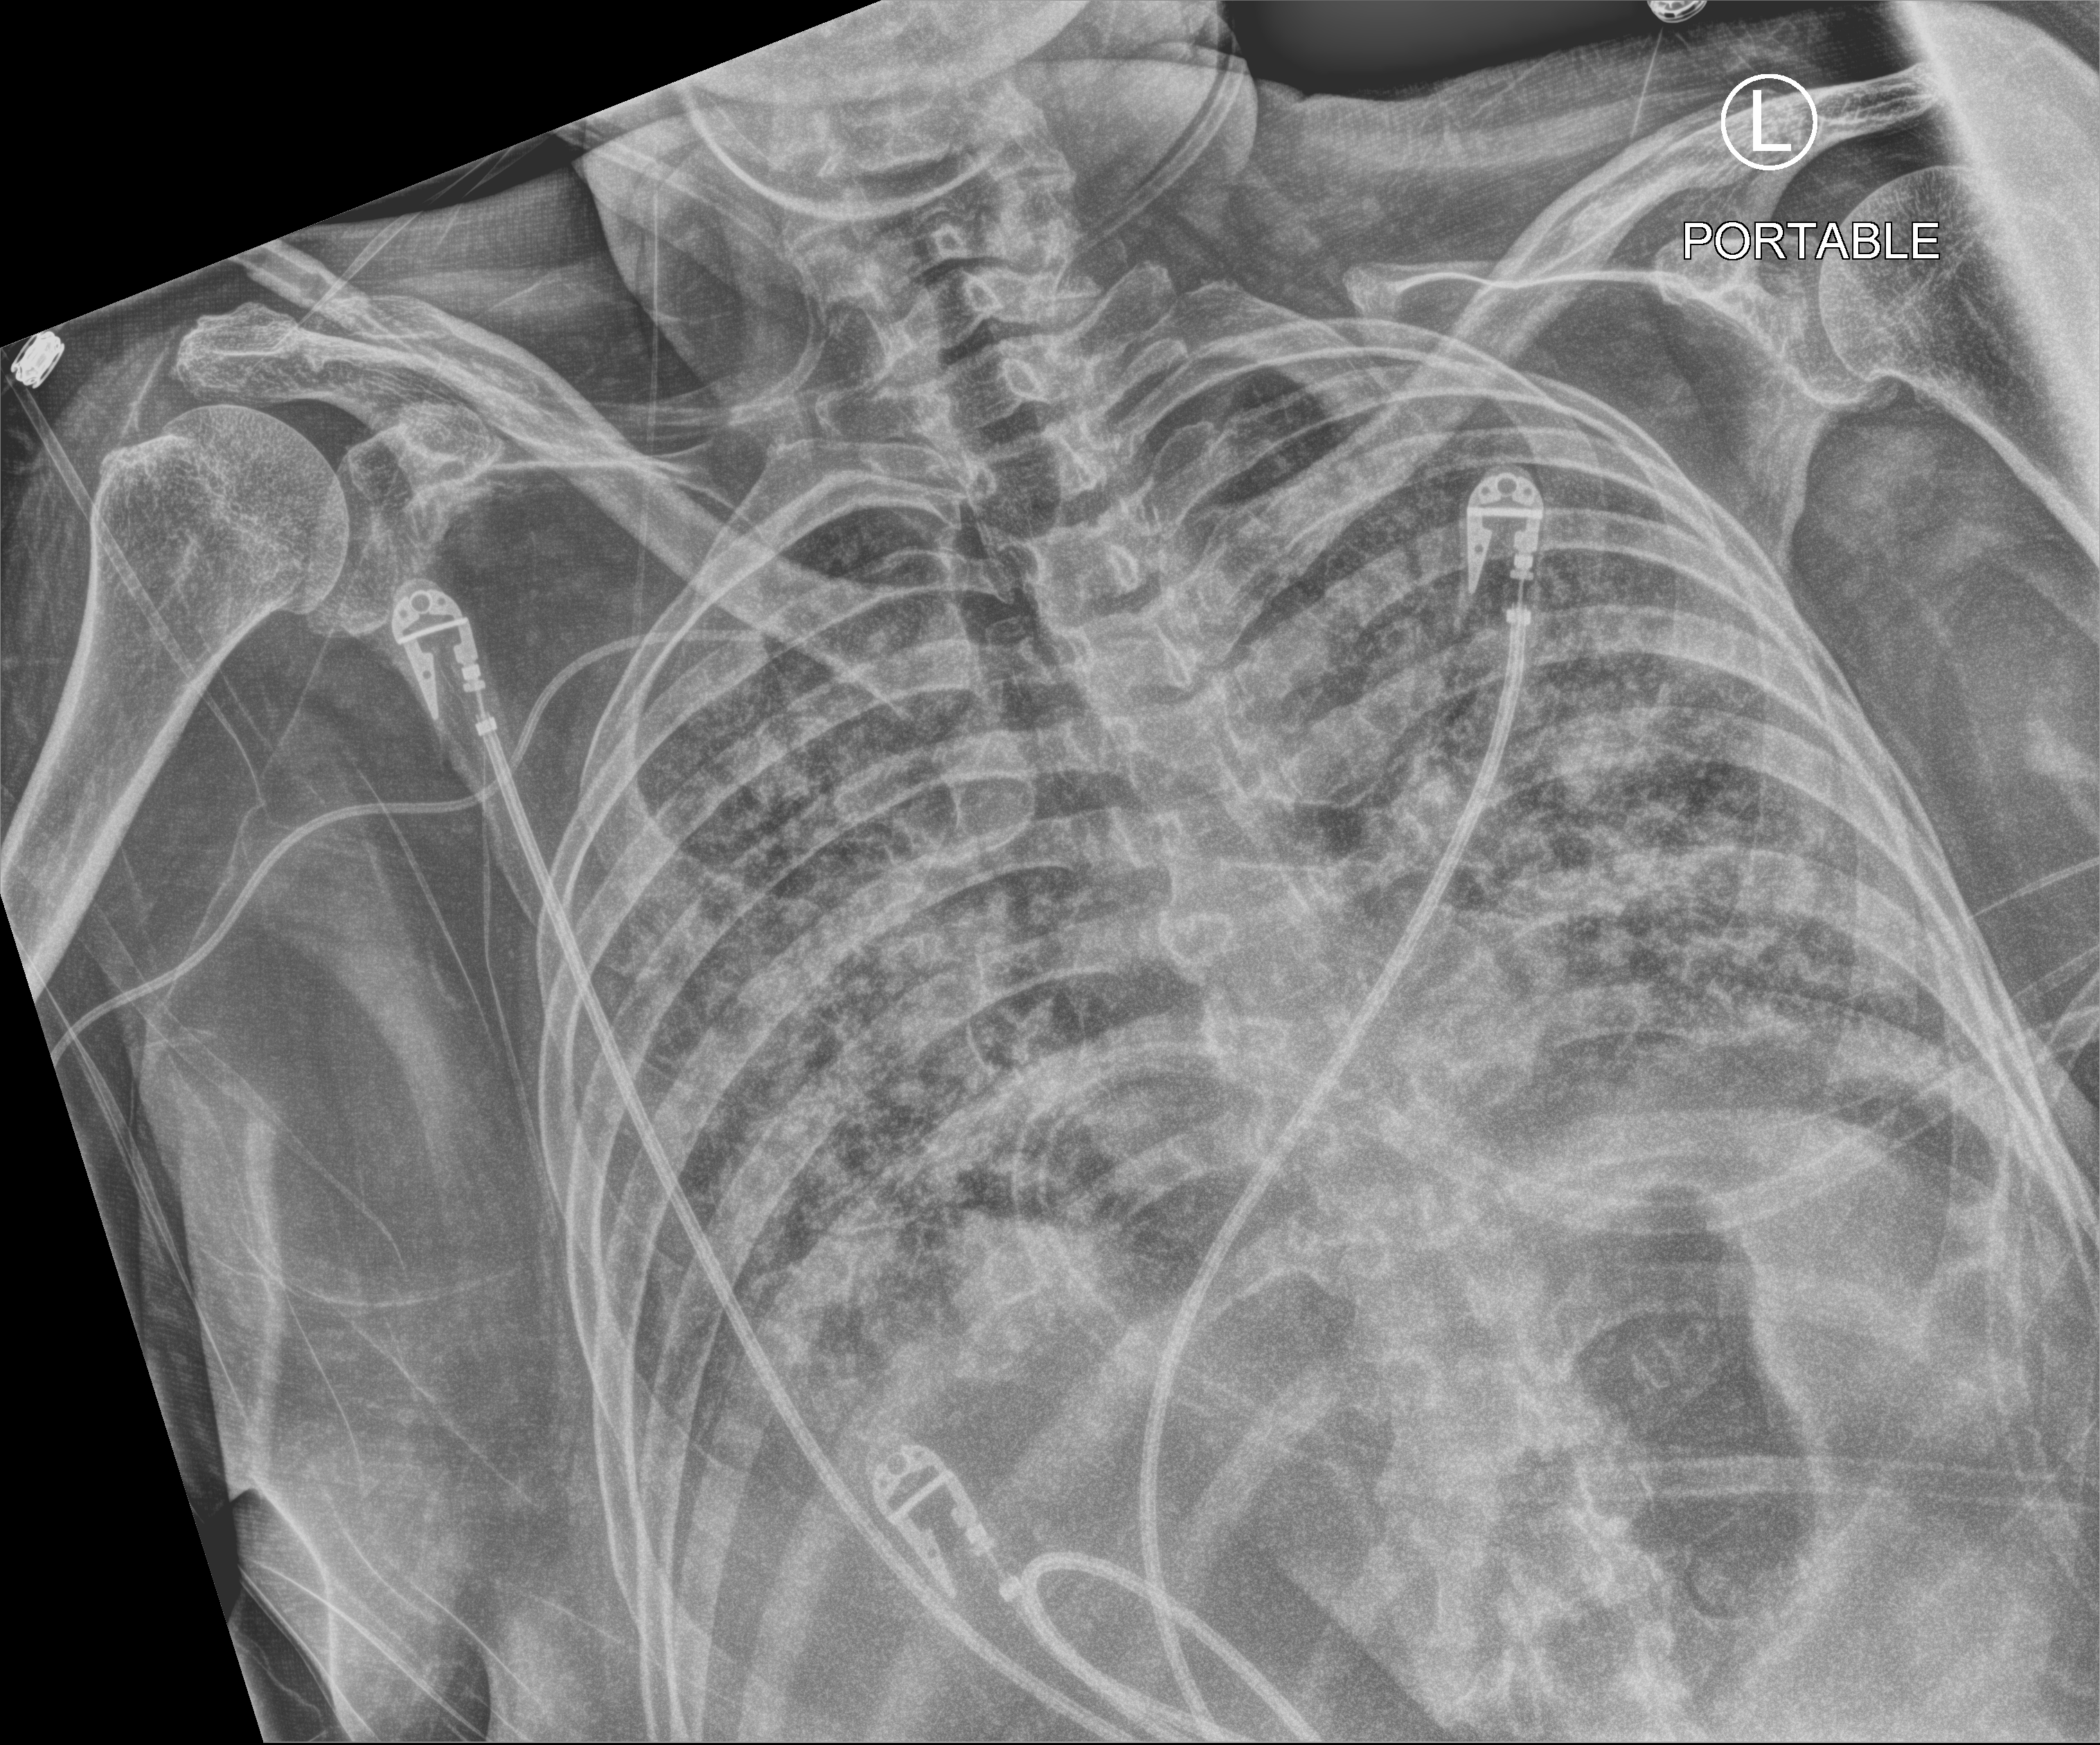
Bedside chest radiograph (computed radiography); anteroposterior (AP) projection. Female patient hospitalised with COVID-19, age 75–90 years.
Hospital-stay facts (about this admission, not read from this image; timing relative to this image not recorded): COPD (admission record): no.